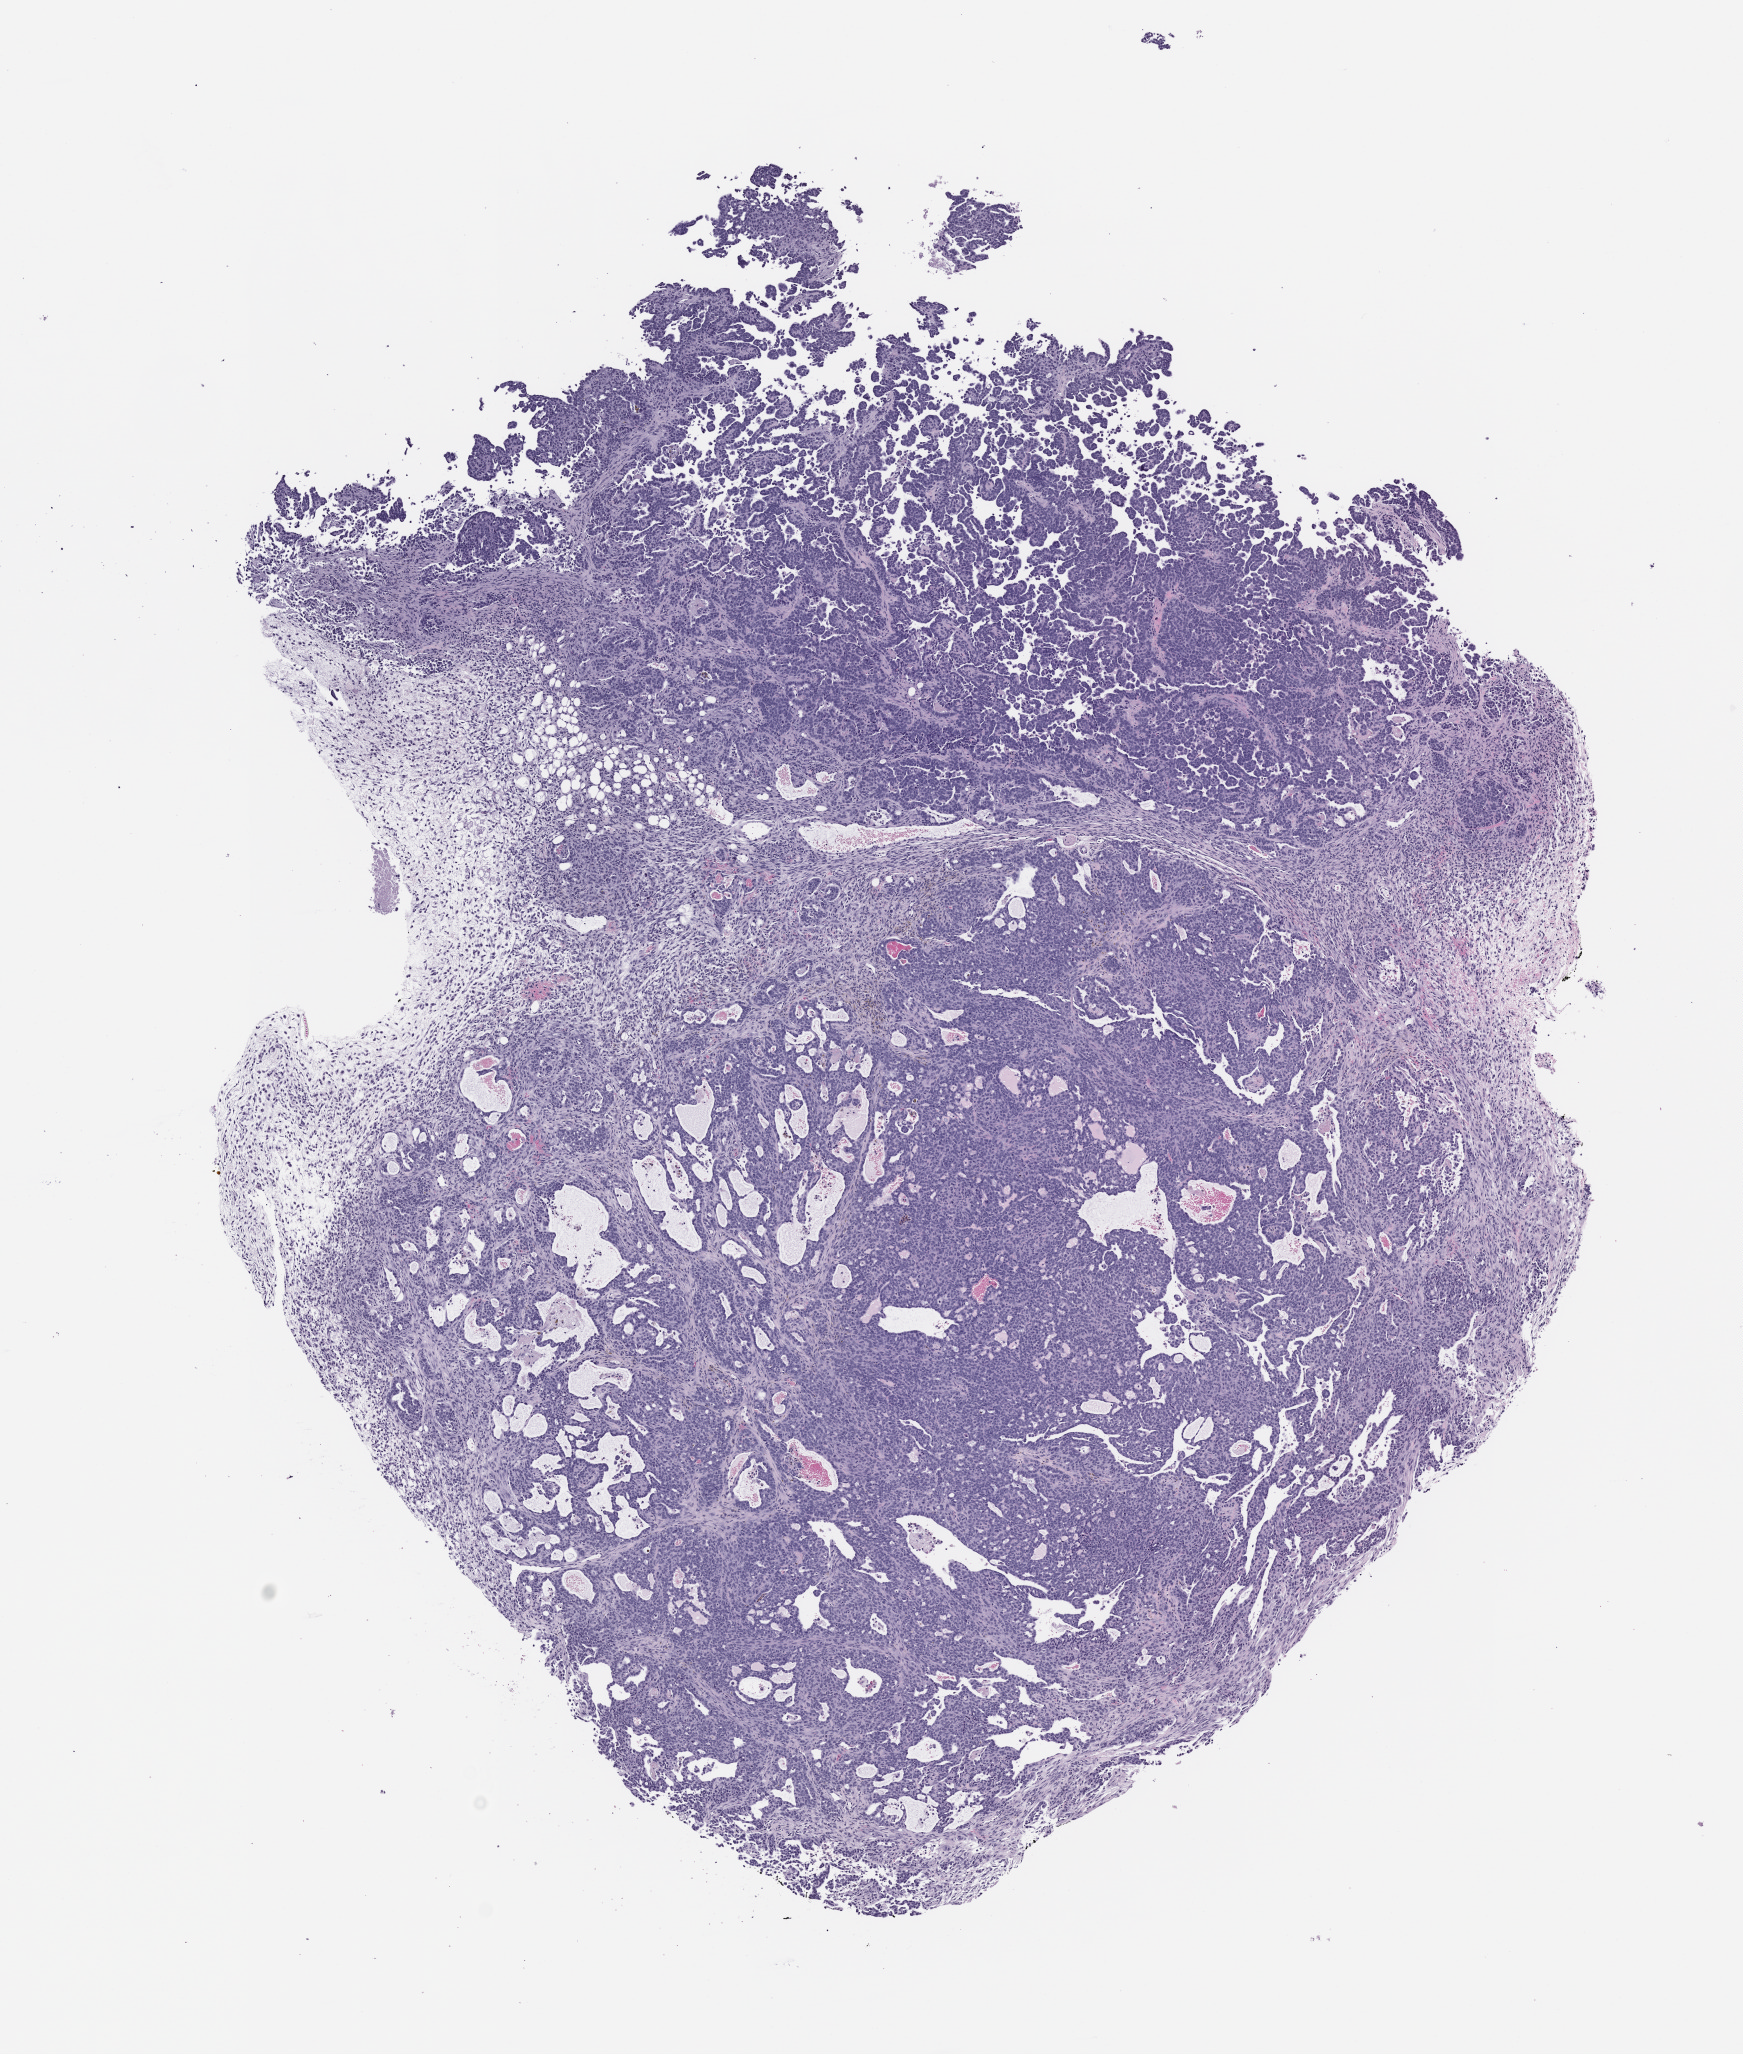
H&E whole-slide image of a patient-derived xenograft (PDX) tumor grown in a mouse, passage 2, shown as a low-resolution overview of the whole scanned area (about 7.0 x 8.3 mm); FFPE section.
Originating patient diagnosis: Mesothelial Neoplasm.